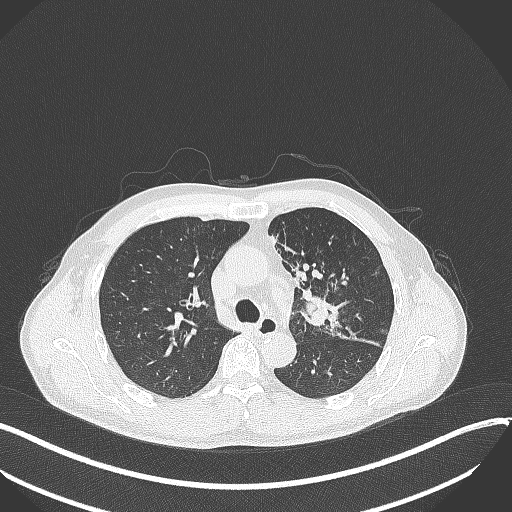
Chest CT, one axial slice. Position 231 of 411 along the scan axis. Reconstruction kernel B70f. Lung window (W 1500 / L -600 HU). 1 mm slice thickness. 512 × 512 image matrix, field of view 400 × 400 mm. Male patient, age 56 years. Case-level facts recorded for this patient, not image findings: clinical TNM (as recorded): T2a N0 M0.
Outlined on this slice (rectangle marked by the reading radiologist):
- lung tumour (recorded histology: squamous cell carcinoma): bounding box (x1, y1, x2, y2) in pixels: (300, 287, 350, 329)